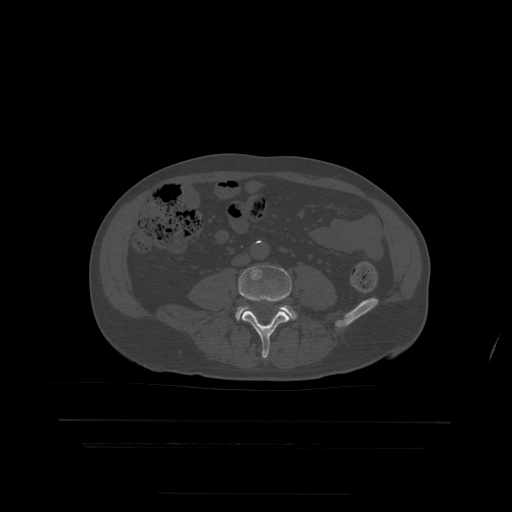
CT including the spine, one axial slice; slice 90 of 522 in the series (ordered by position); bone window (W 1800 / L 400 HU); 512 × 512 image matrix, field of view 436 × 436 mm. Patient age 68 years. Case-level facts recorded for this patient, not image findings: primary cancer: urothelial.
Annotated regions visible in this slice (semi-automatic segmentation, software-assisted and operator-edited):
- L4 vertebra: bounding box (x1, y1, x2, y2) in pixels: (239, 266, 293, 358)
- L5 vertebra: (236, 306, 297, 320)